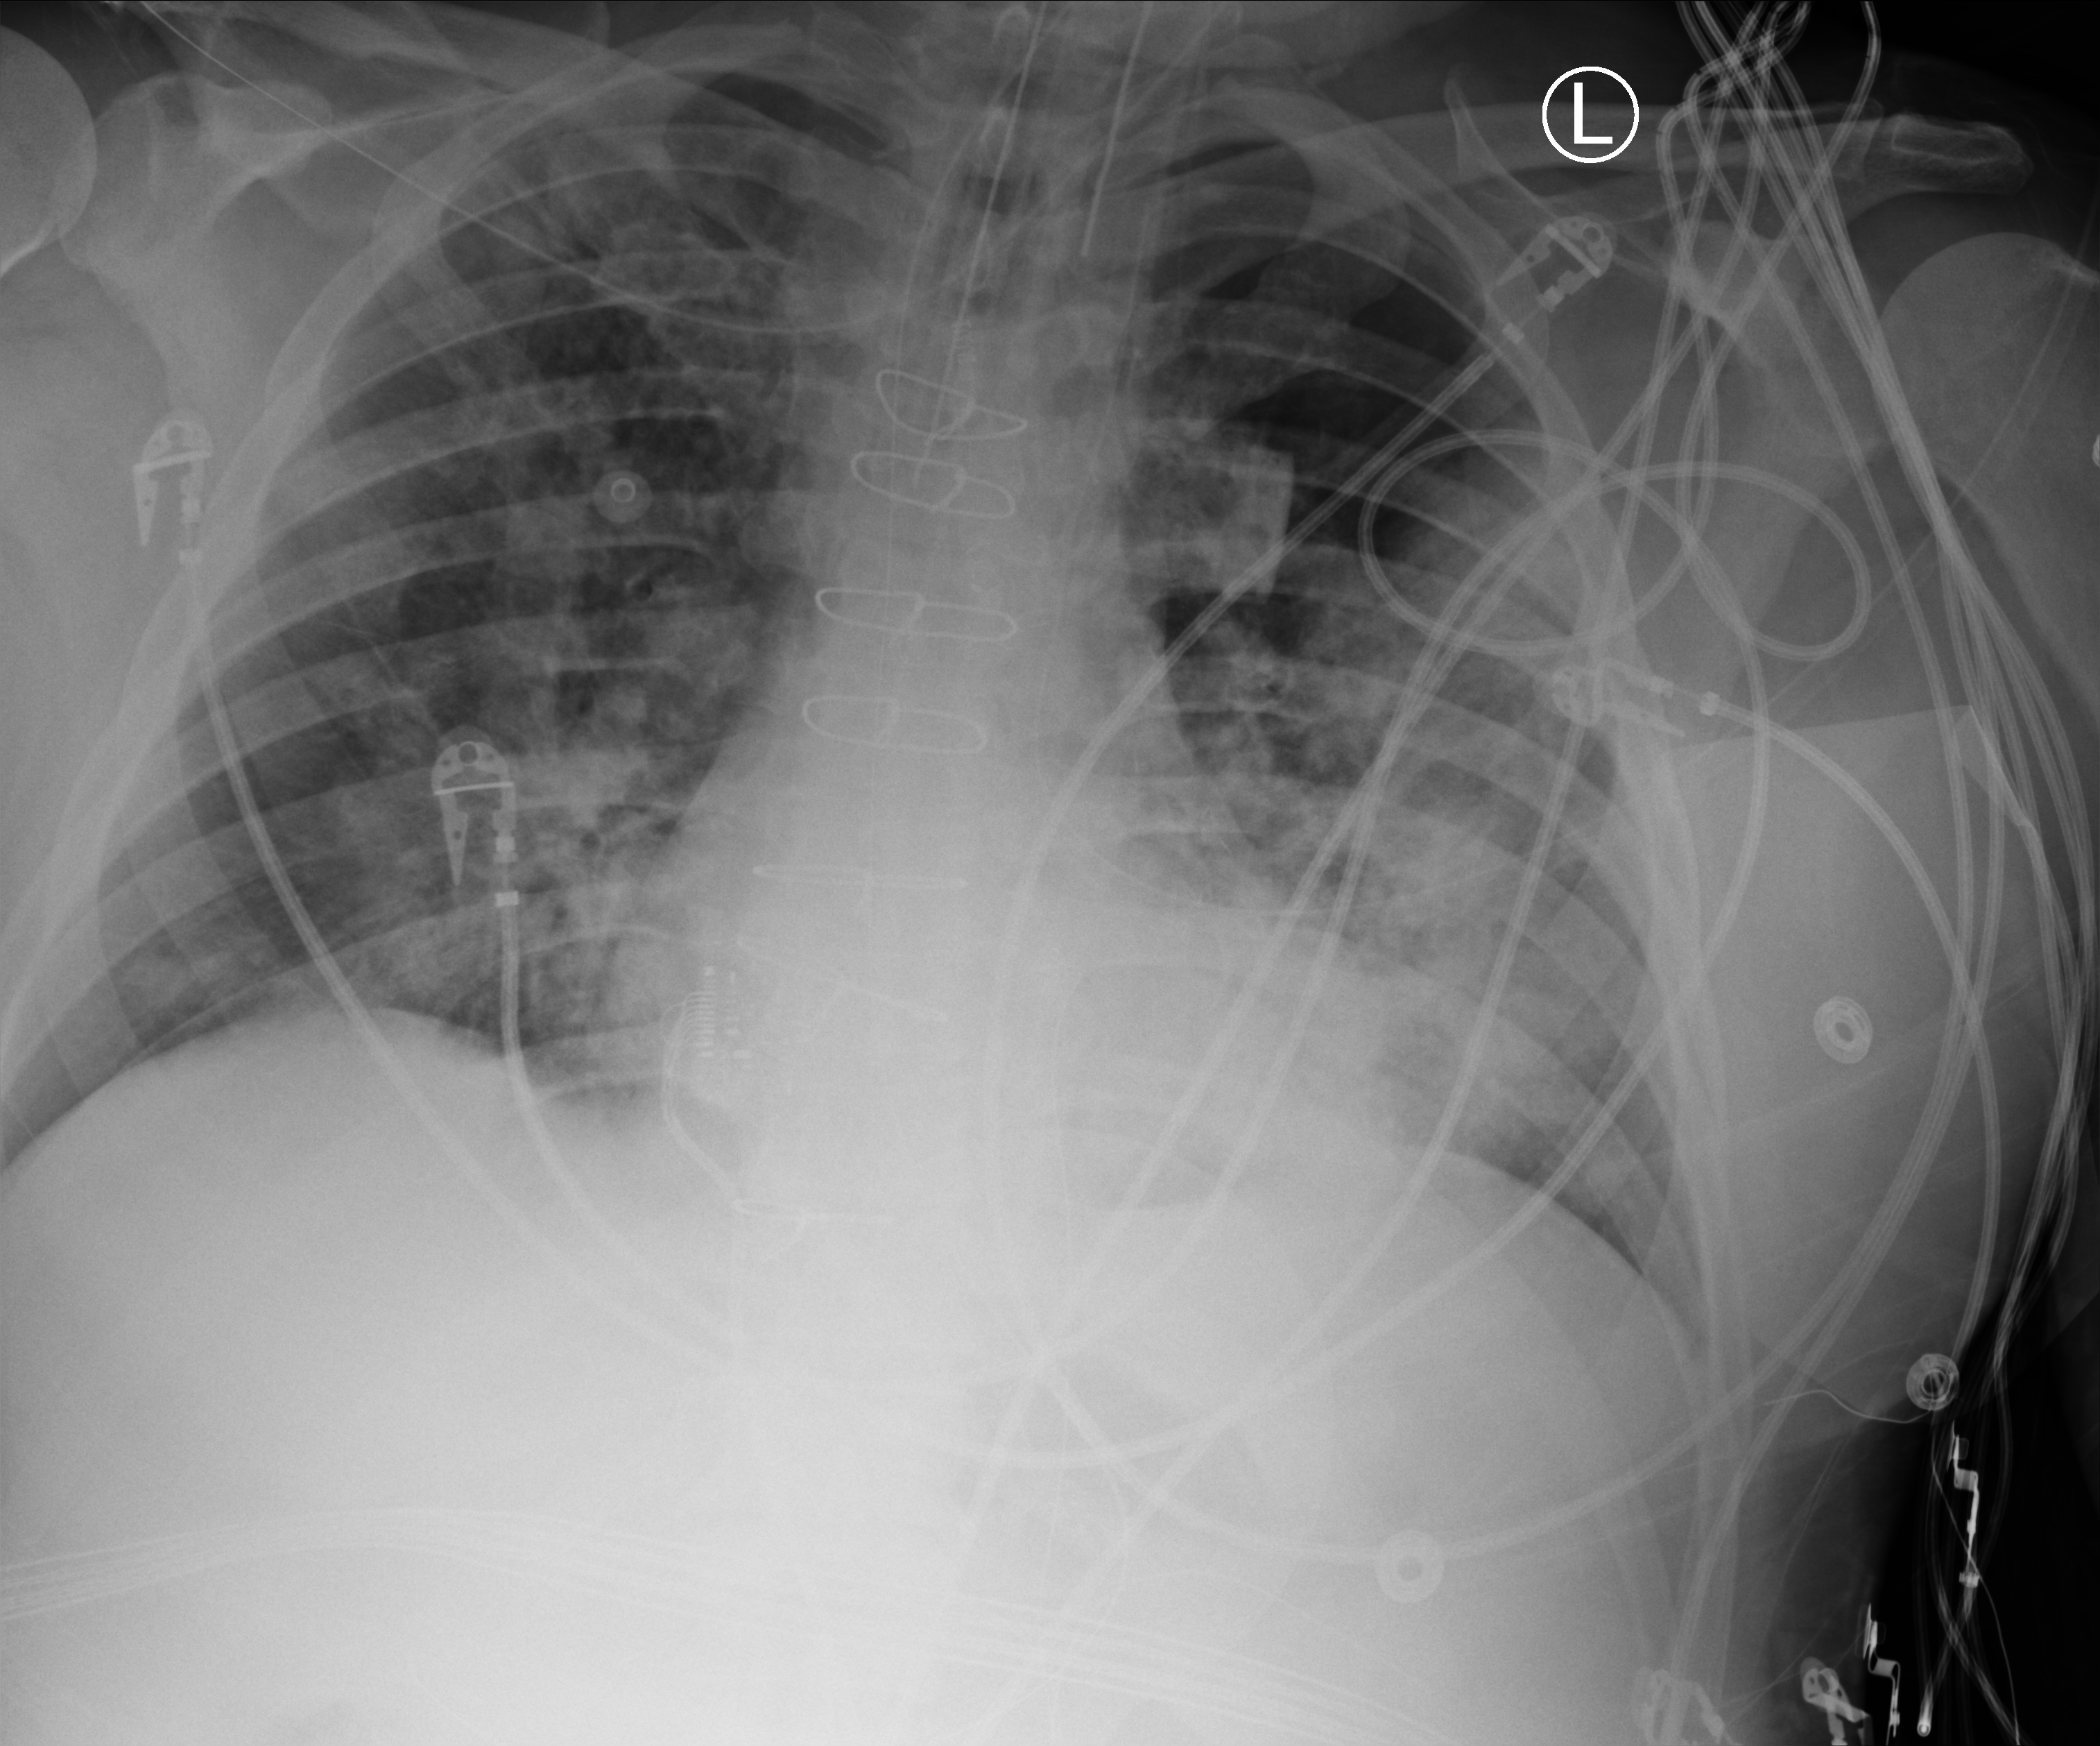
Portable chest radiograph, anteroposterior (AP) projection. Patient hospitalised with COVID-19; male, aged 60–74 years.
From the hospital-stay record, not from the radiograph (when in the stay this image was taken is not recorded):
- admitted to intensive care during this hospital stay: yes